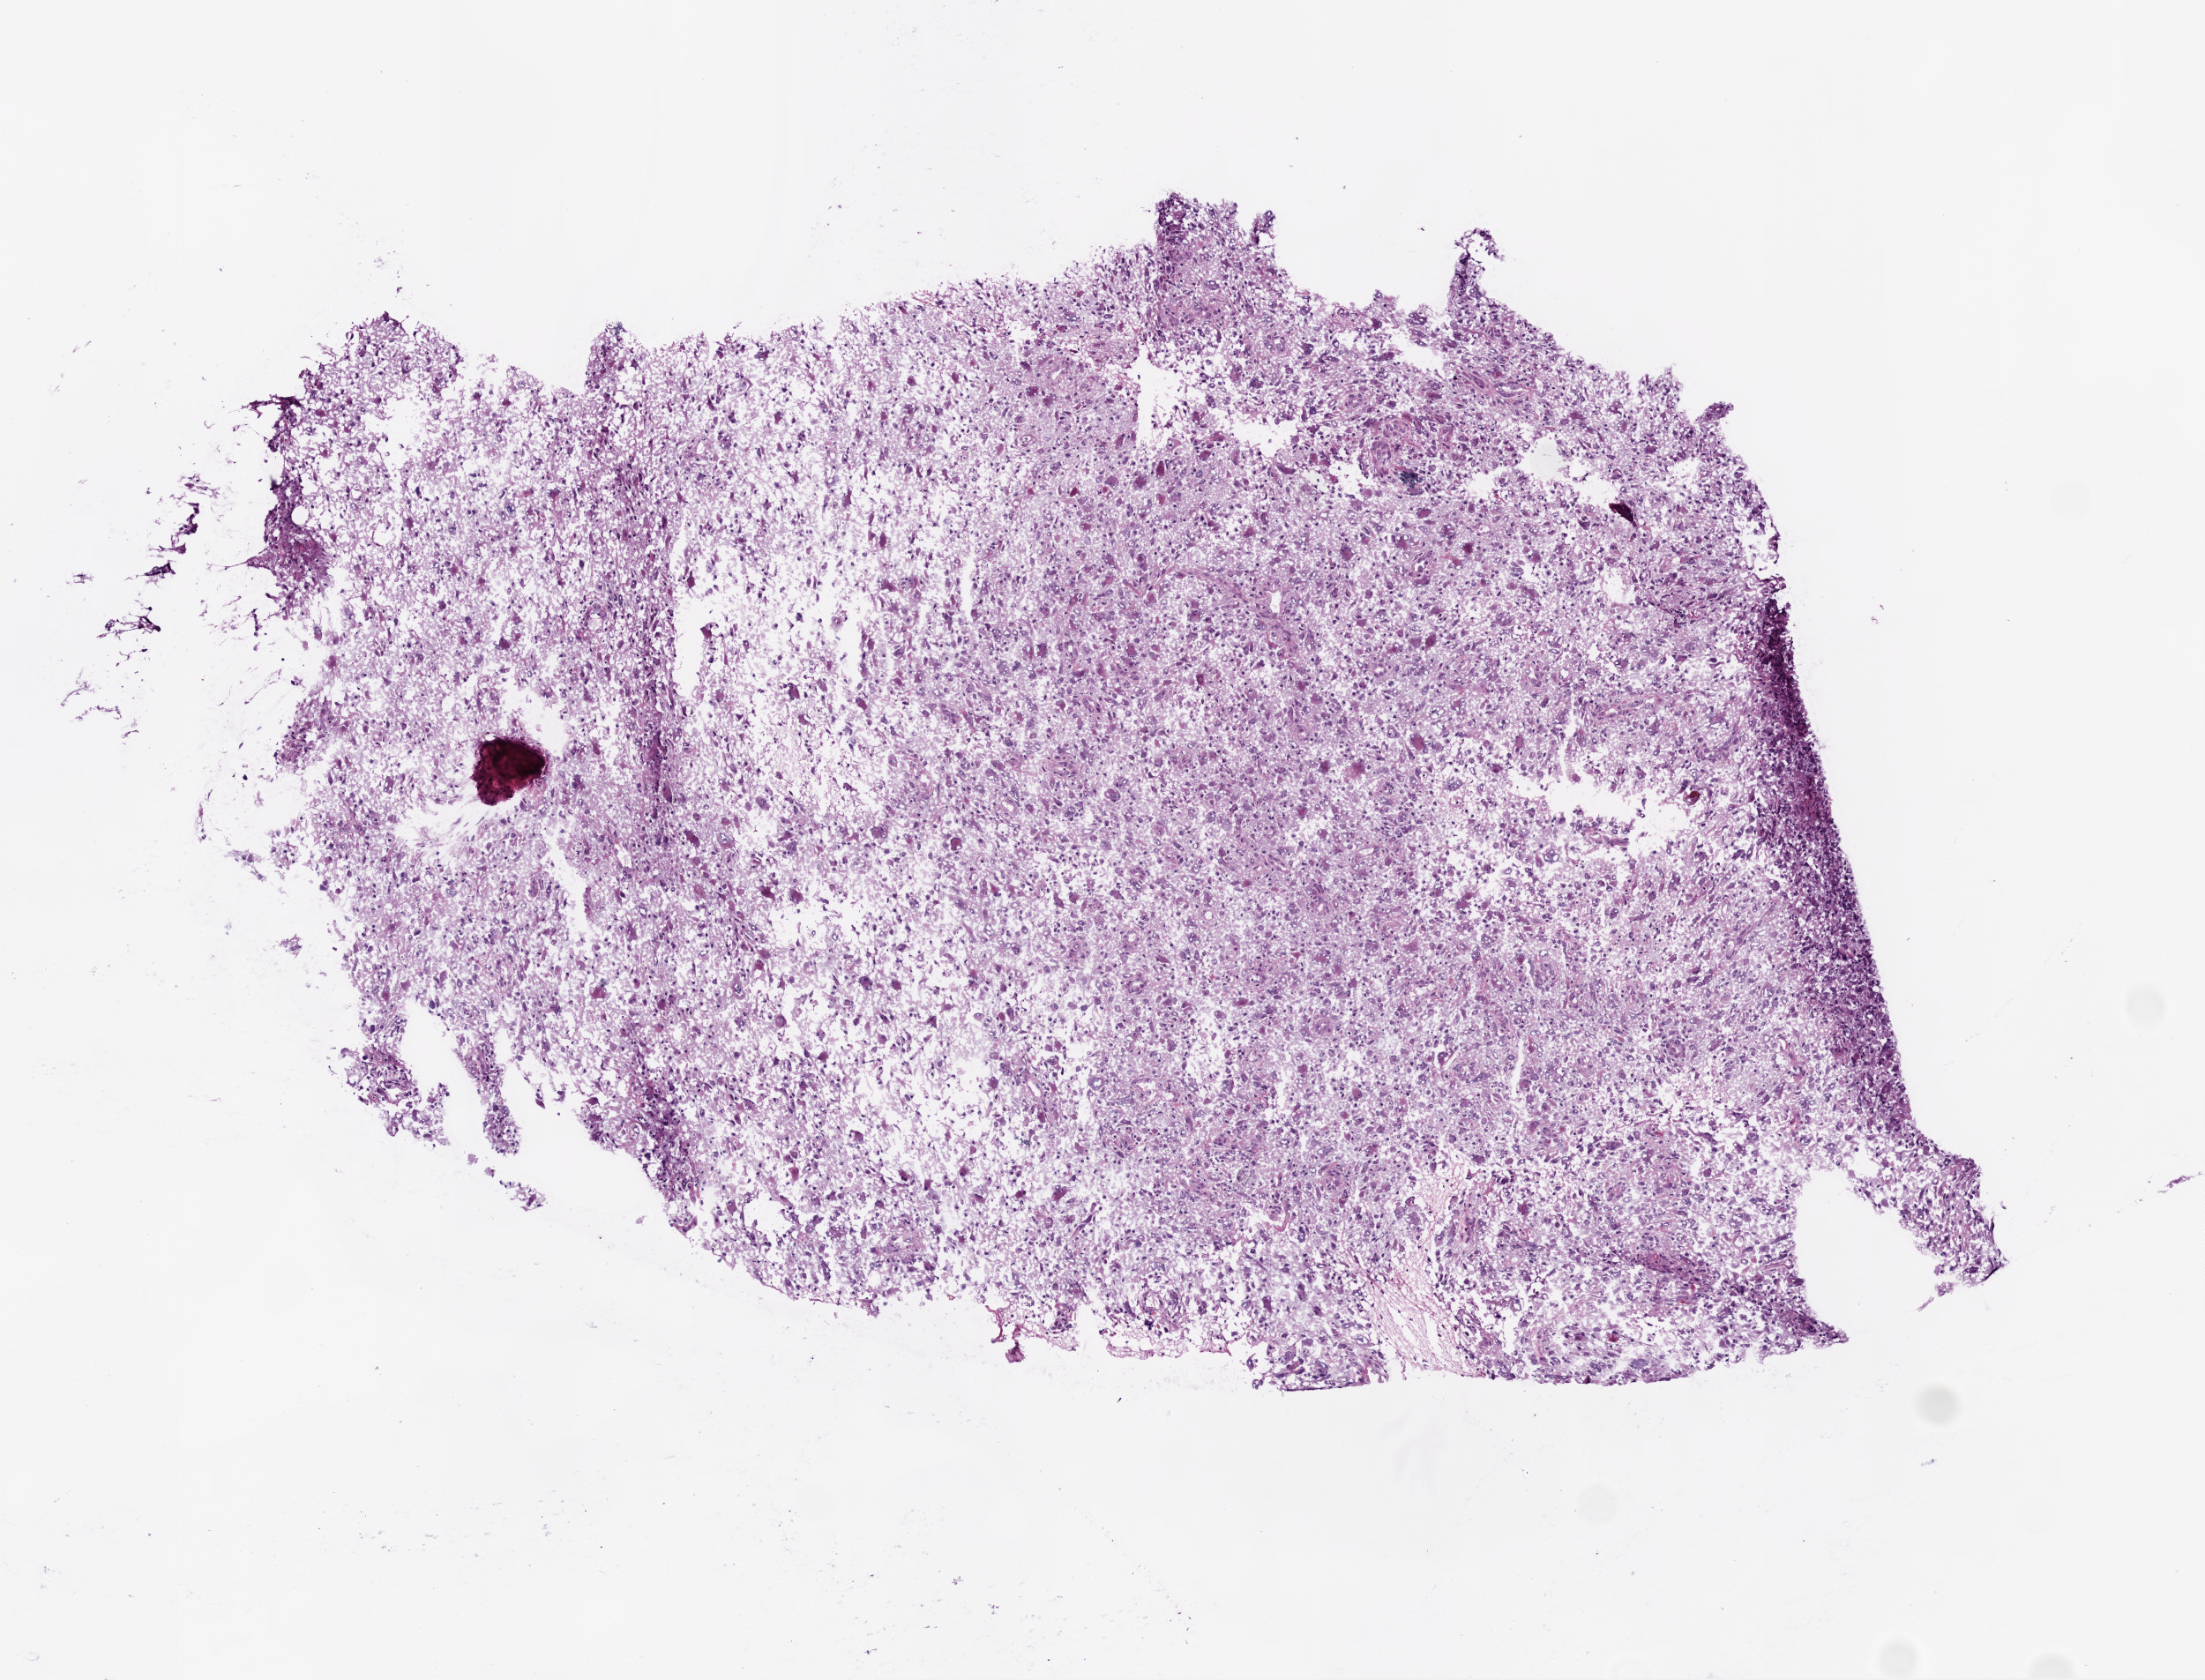
Hematoxylin and eosin (H&E) stained whole-slide image — whole scanned area (about 5.0 x 3.8 mm, acquisition: 20x scan) shown as a low-resolution overview. Frozen section from the bottom of the tissue portion. Primary tumour sample from the brain. Male patient; age at initial diagnosis 63 years. Slide review estimates, as recorded: tumour cells 93%, tumour nuclei 85%.
Histologic diagnosis: Glioblastoma.